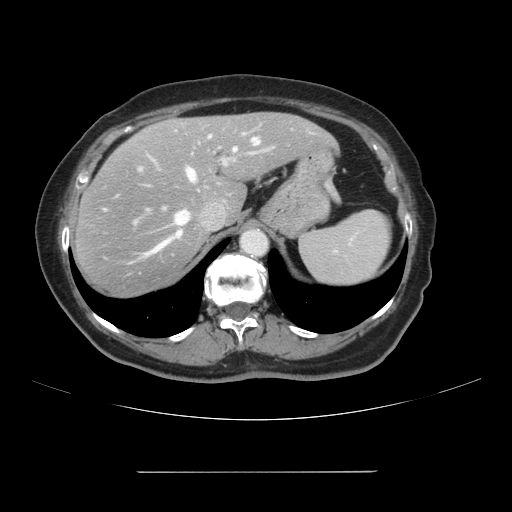
Contrast-enhanced abdominal CT, one axial slice. Position 78 of 111 along the scan axis. Intravenous contrast given. Soft-tissue window (W 400 / L 40 HU). 2.5 mm slice thickness. 512 × 512 image matrix, field of view 400 × 400 mm. Female patient, age 74 years. Case-level facts recorded for this patient, not image findings: diagnosis: colorectal cancer liver metastases, imaged before liver resection; multiple liver metastases: yes; largest metastasis: 1.1 cm; disease in both lobes: yes.
Outlined on this slice (expert manual segmentation):
- hepatic veins: bounding box [x1, y1, x2, y2] px = [105, 138, 259, 265]
- liver: [72, 113, 333, 297]
- planned liver remnant (the part of the liver to remain after resection): [158, 113, 333, 220]
- portal vein (with intrahepatic branches): [139, 134, 244, 171]